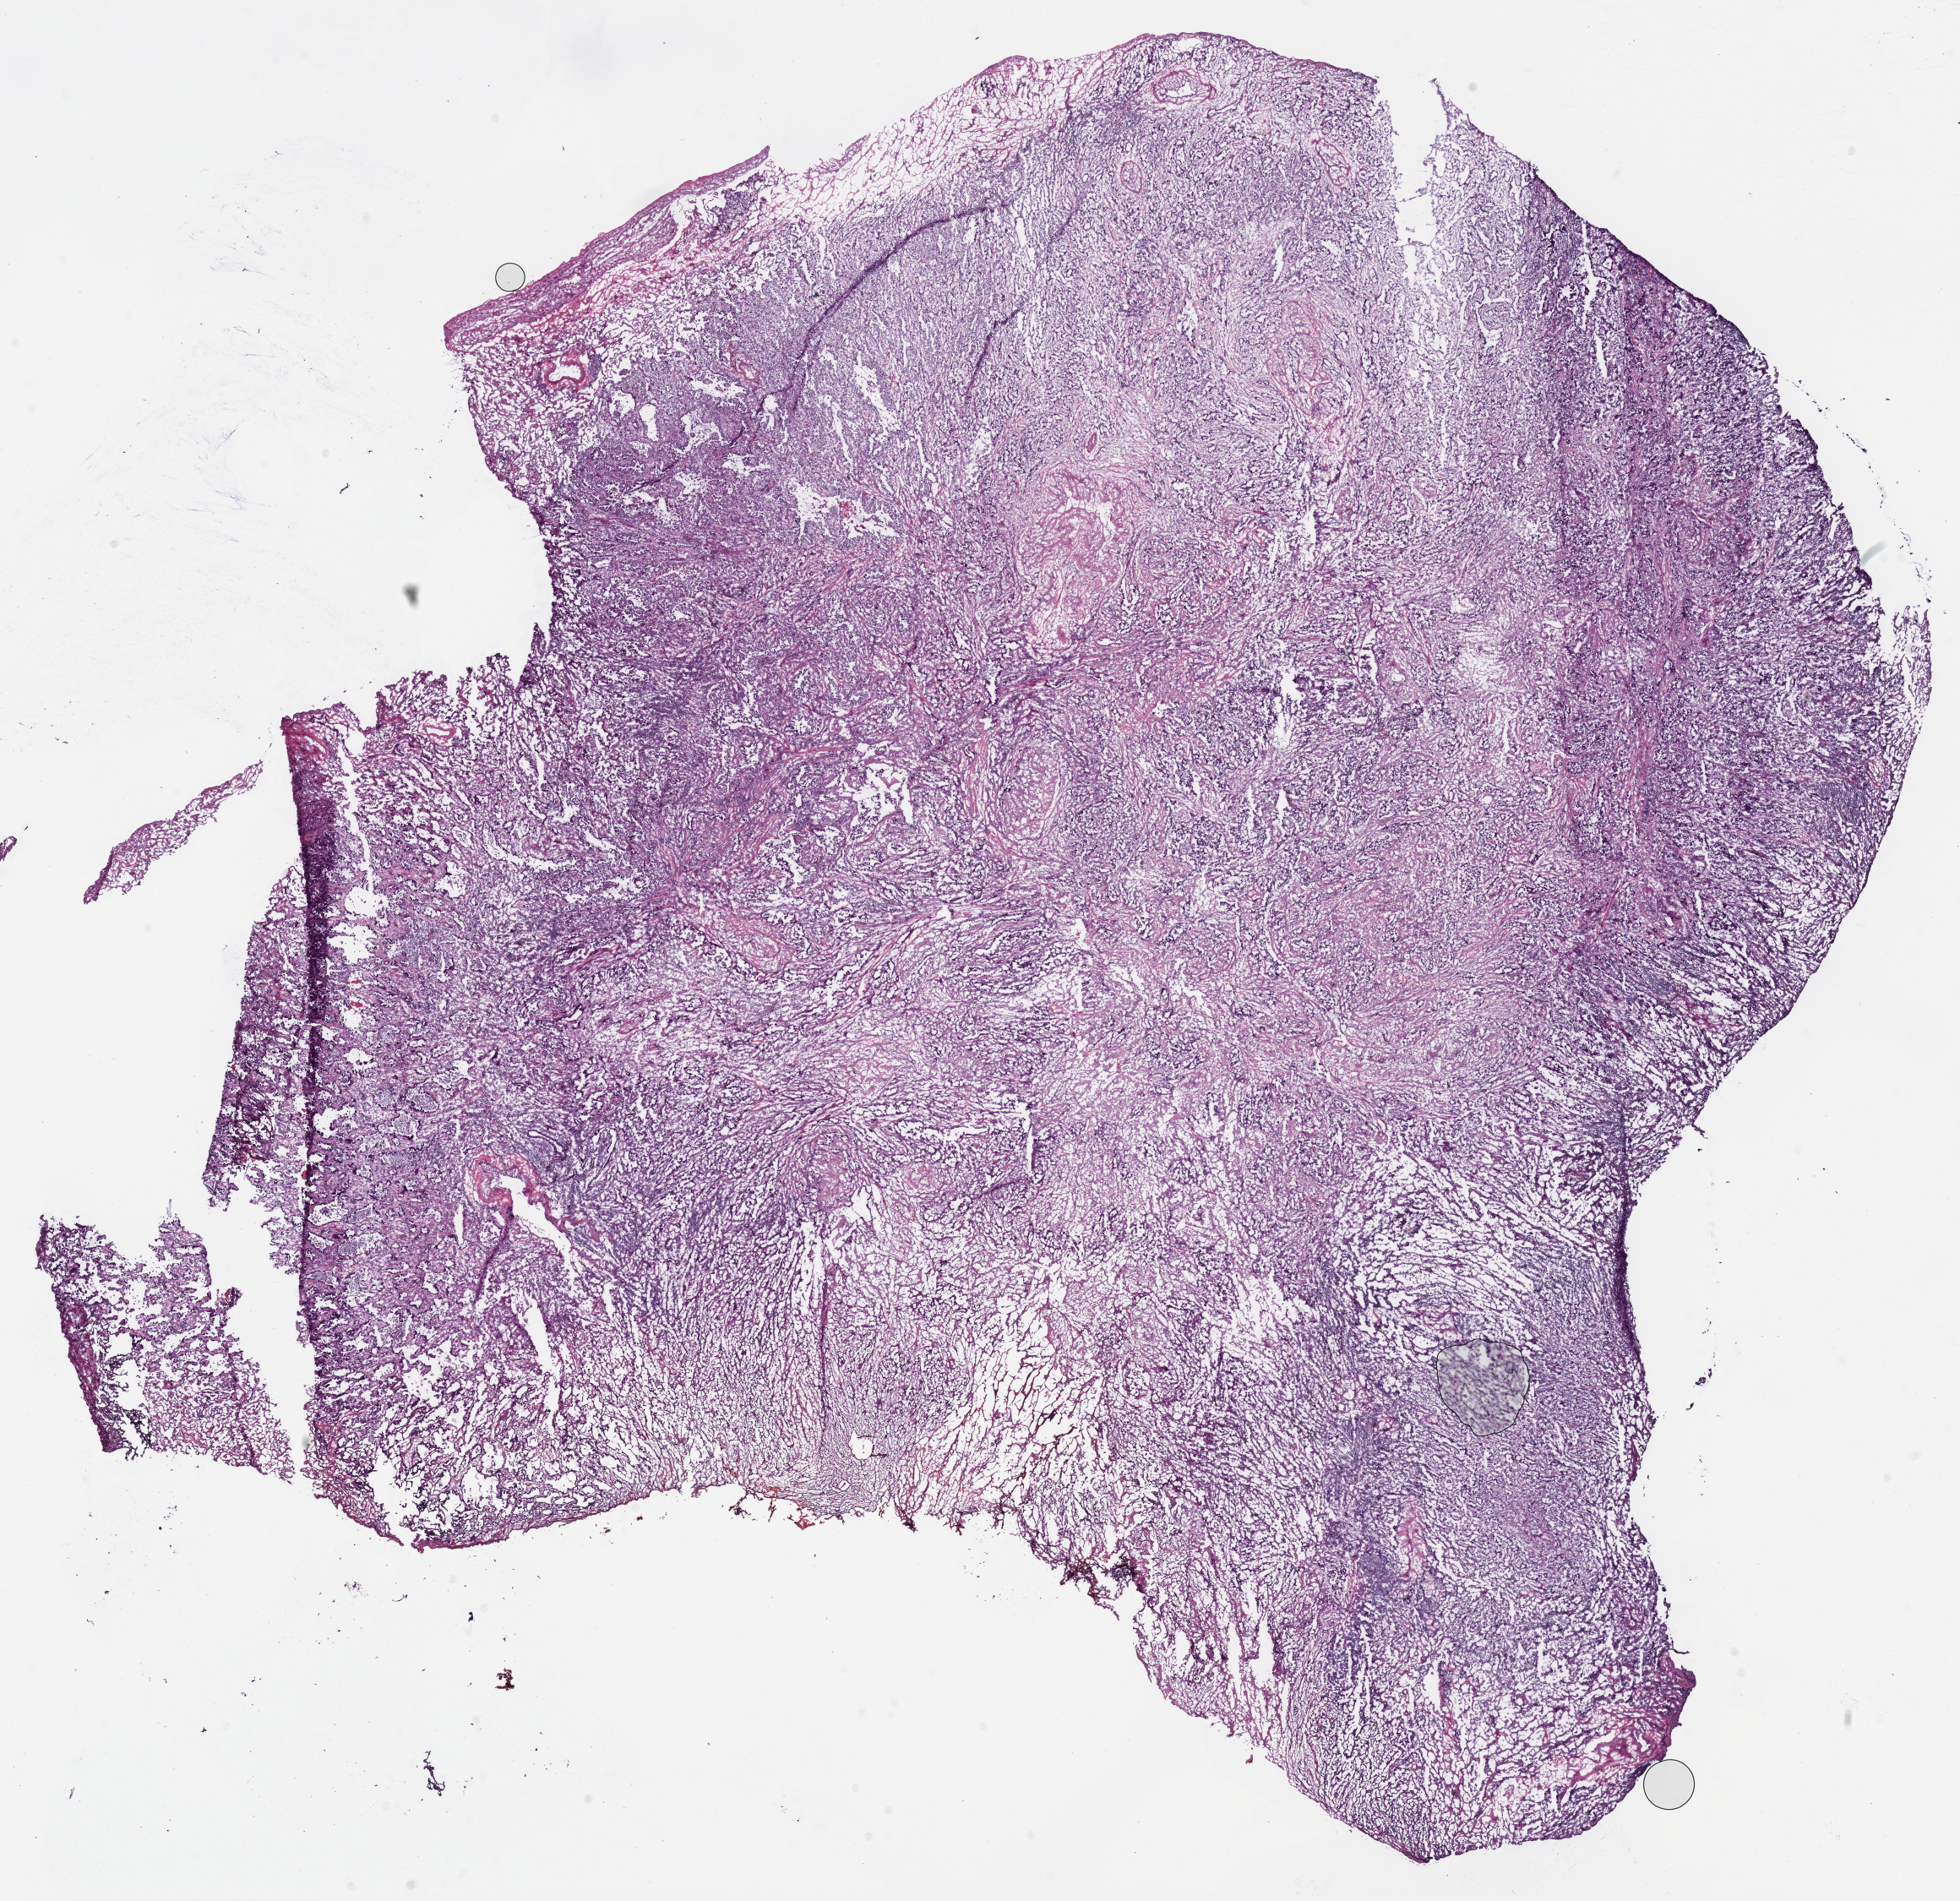
Digitized Hematoxylin and eosin (H&E) stained tissue section (whole slide) — low-resolution overview of the scanned area, about 18.3 x 17.7 mm, frozen section, sample: primary tumour, lung. Female patient; age at initial diagnosis 66 years. Slide review estimates, as recorded: tumour cells 75%, tumour nuclei 70%, normal cells 0%, stromal cells 25%, necrosis 0%. Infiltration values recorded for this section: lymphocyte infiltration 15%, monocyte infiltration 0%, neutrophil infiltration 0%.
* TNM: T2 N0 M0
* pathologic diagnosis: Adenocarcinoma, NOS
* AJCC pathologic stage: IB (7th edition)